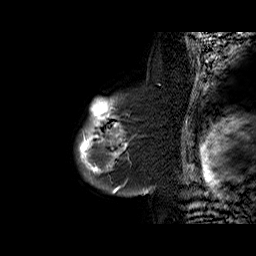
Breast MRI (dynamic contrast-enhanced), one sagittal slice; slice 49 of 60 in the series (ordered by position); dynamic contrast-enhanced series, time point 2 of 6 at this slice position (early post-contrast); 1.5 T; TE 6.3 ms, TR 32.4 ms; 4 mm slice thickness; 256 × 256 image matrix, field of view 200 × 200 mm. Female patient. Case-level facts recorded for this patient, not image findings: setting: breast cancer imaged before/during neoadjuvant chemotherapy; receptor status: triple-negative.
Annotated regions visible in this slice (semi-automatic segmentation, software-assisted and operator-edited):
- analysis volume of interest (the breast-tissue region the enhancement analysis was run in; not a lesion): bounding box [x1, y1, x2, y2] px = [75, 95, 160, 187]
- tumour enhancement mask (voxels above the 100 % enhancement threshold inside the analysis volume of interest): [79, 99, 126, 173]